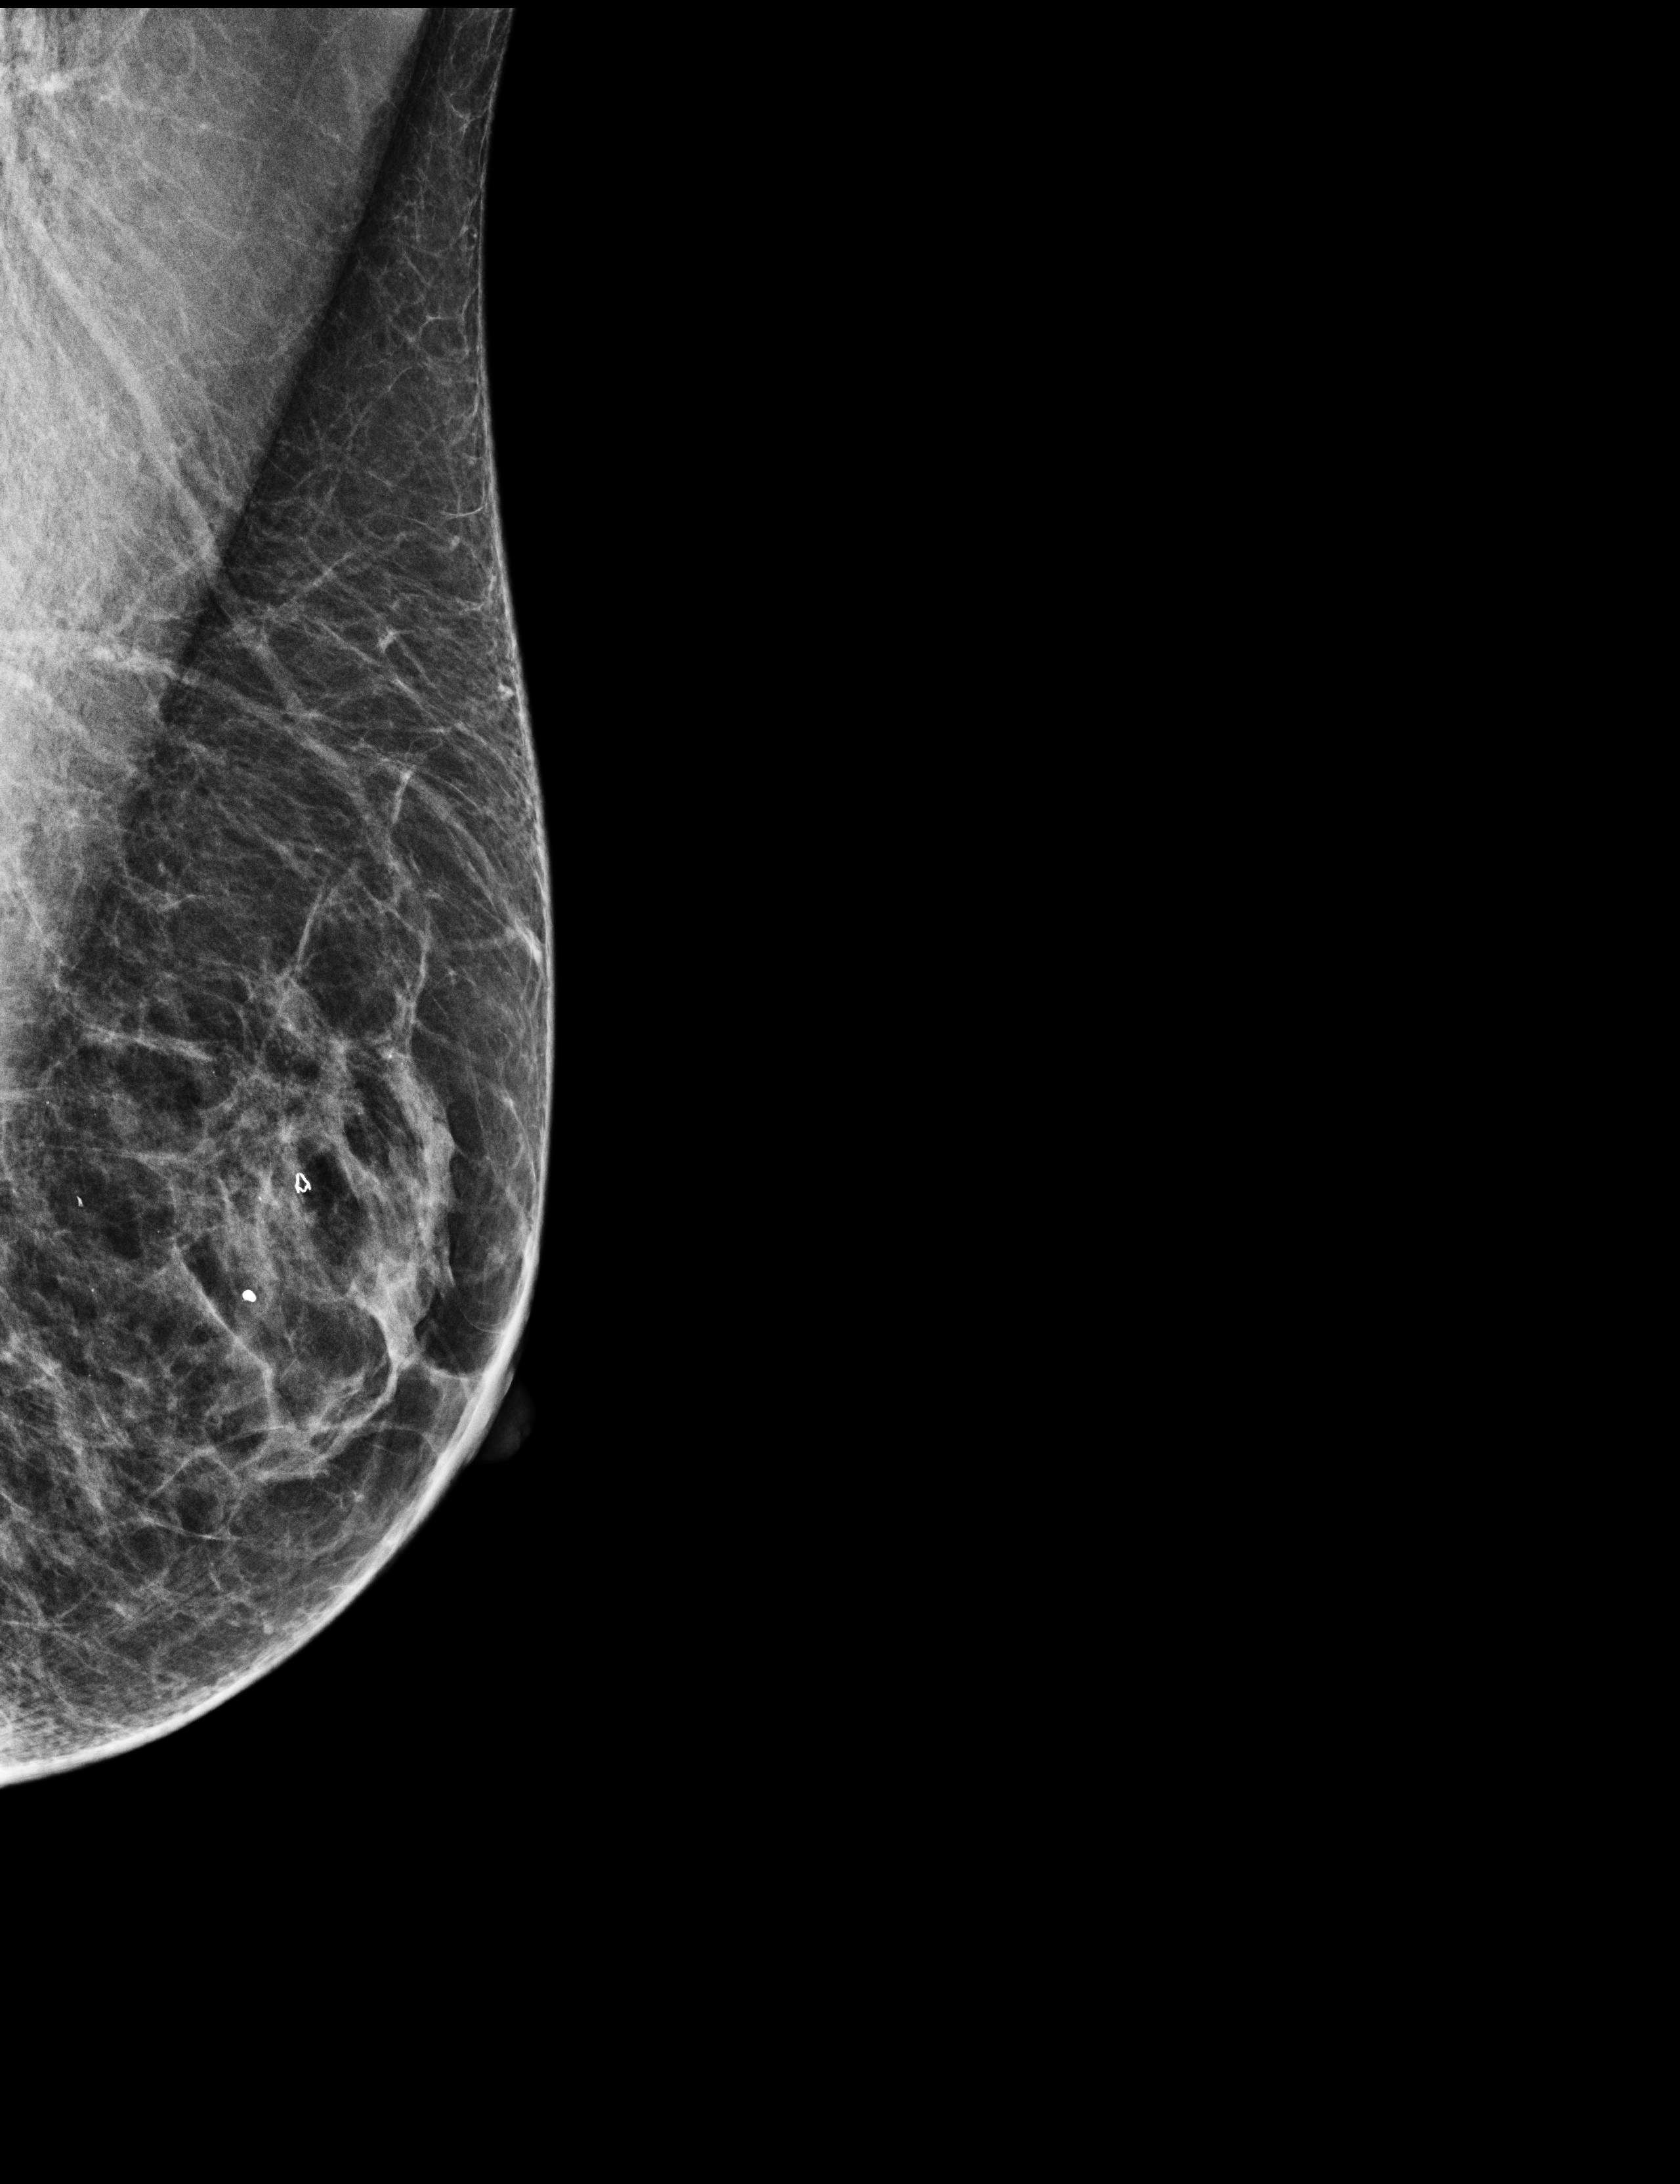
Annual screening mammography examination; compressed breast thickness 39 mm. Female patient, age 68 years.
Image type: full-field digital mammogram. Breast: left. Projection: medio-lateral oblique projection.